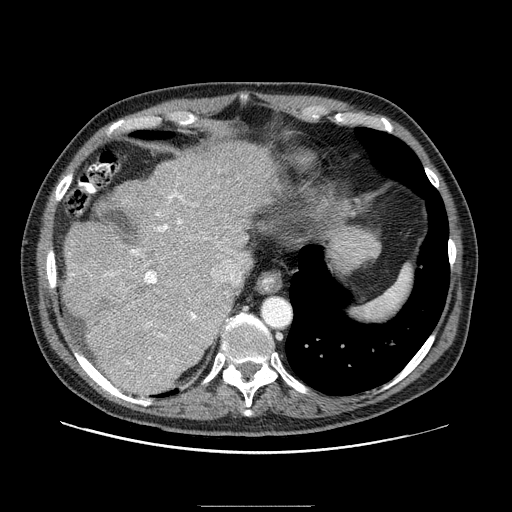
Contrast-enhanced abdominal CT (liver protocol), one axial slice. One of 2 acquisitions stored at this slice position. Soft-tissue window (W 400 / L 40 HU). 2.5 mm slice thickness. 512 × 512 image matrix, field of view 400 × 400 mm. Case-level facts recorded for this patient, not image findings: diagnosis: hepatocellular carcinoma (patient treated with transarterial chemoembolisation; whether this scan precedes or follows treatment is not stated here); TNM stage (as recorded): Stage-II; Child-Pugh class: A; tumour nodularity: multinodular; tumour size: 3.2 cm.
Structures marked on this image (semi-automatic segmentation, software-assisted and operator-edited):
- abdominal aorta: bounding box <263,298,291,326> (left, top, right, bottom; pixels)
- liver parenchyma outside the tumour (the mass and vessels are separate outlines, so this box may not span the whole liver): <60,142,279,394>
- liver vessels: <104,192,232,367>